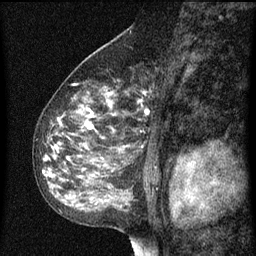
Breast MRI (dynamic contrast-enhanced), one sagittal slice; slice 44 of 60 in the series (ordered by position); dynamic contrast-enhanced series, image 2 of 3 at this slice position (ordered by acquisition); 1.5 T; TE 4.2 ms, TR 8 ms; 256 × 256 image matrix, field of view 180 × 180 mm. Female patient, age 55 years.
Outlined on this slice (semi-automatically segmented with operator editing):
- analysis volume of interest (the breast-tissue region the enhancement analysis was run in; not a lesion): box from (x=36, y=68) to (x=157, y=151) px
- tumour enhancement mask (voxels above the 70 % enhancement threshold inside the analysis volume of interest): (x=52, y=92)–(x=151, y=151)